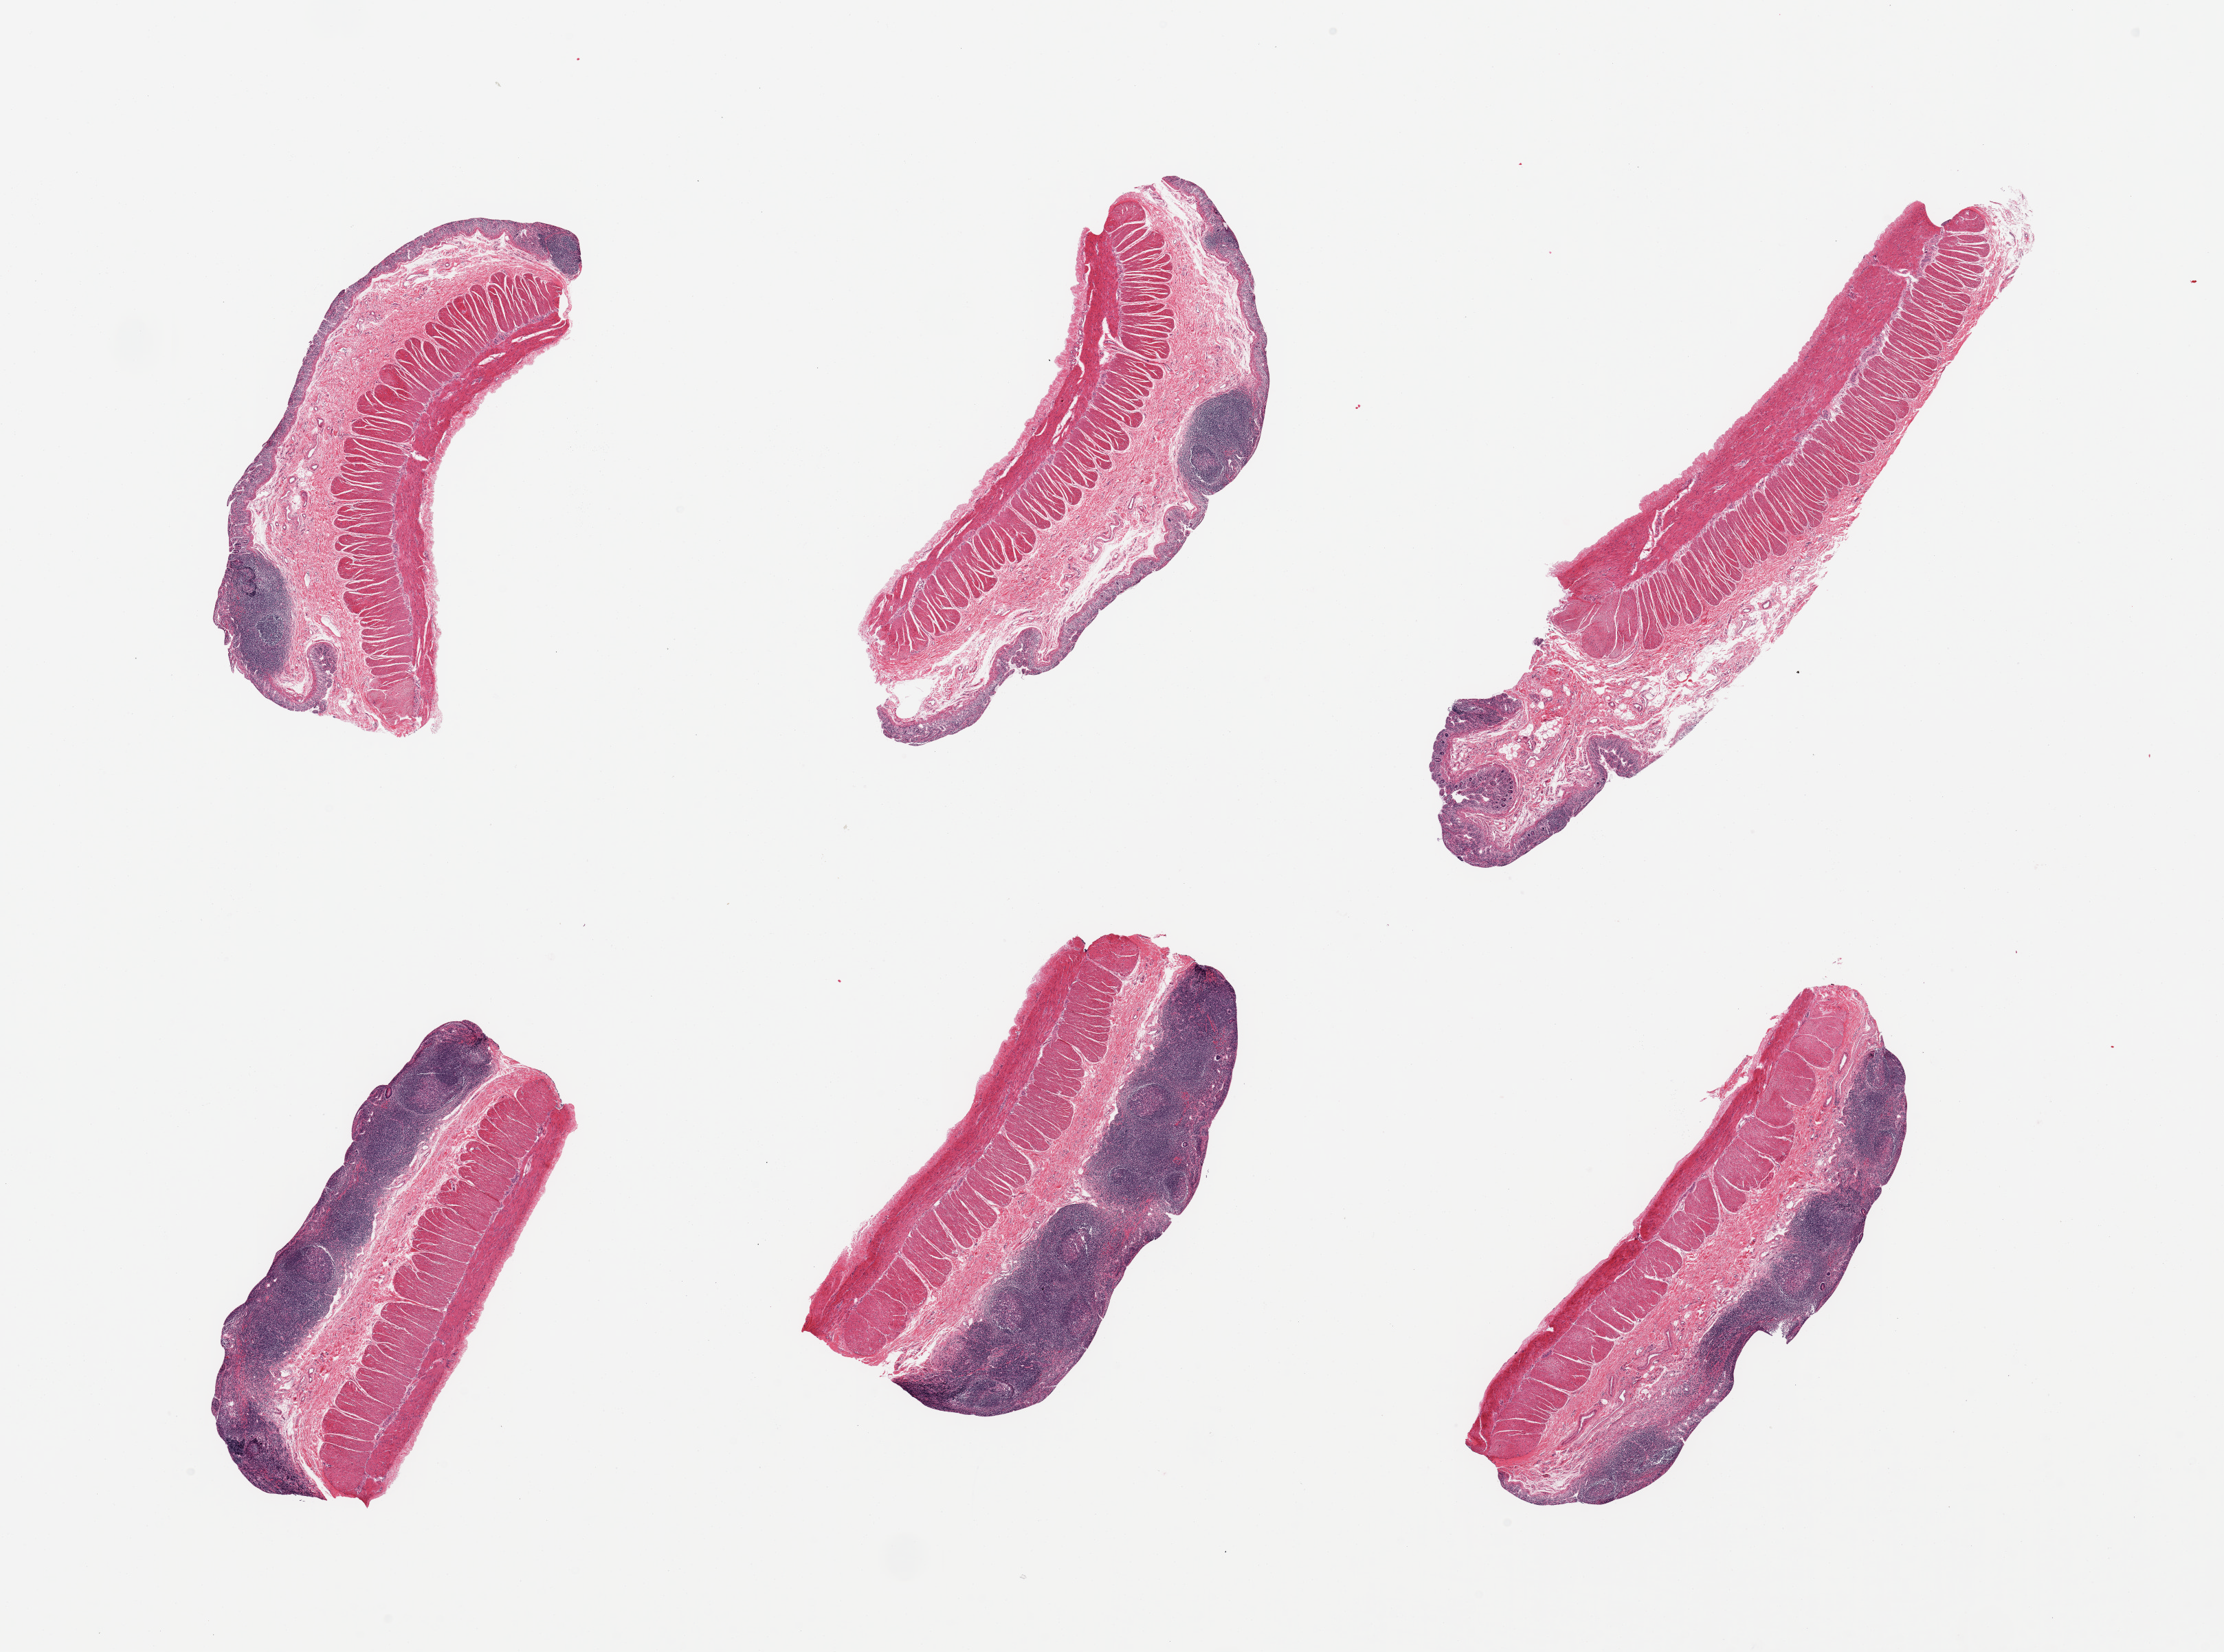
Digitized H&E-stained section, brightfield, shown as a low-resolution overview of the whole scanned area (about 25.6 x 19.0 mm), PAXgene-fixed, paraffin-embedded tissue, target tissue: ileum, tissue donor sample. Donor: male.
* reviewer comment on this tissue sample: 6 pieces; muscularis (not target) and partially autolyzed mucosa, 3 pieces have good lymphoid component